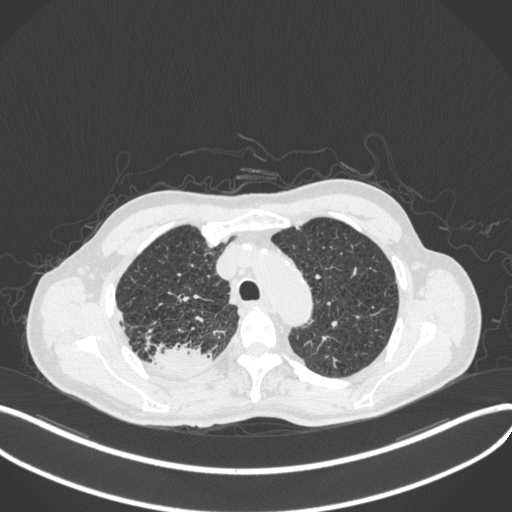
Chest CT, one axial slice. Position 342 of 423 along the scan axis. Reconstruction kernel B31f. 120 kVp. Lung window (W 1500 / L -600 HU). 512 × 512 image matrix, field of view 400 × 400 mm. Male patient, age 79 years. Case-level facts recorded for this patient, not image findings: clinical TNM (as recorded): T3 N0 M0.
Structures marked on this image (rectangle marked by the reading radiologist):
- lung tumour (recorded histology: adenocarcinoma): bounding box <149,345,214,377> (left, top, right, bottom; pixels)